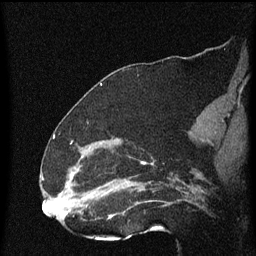
Breast MRI (dynamic contrast-enhanced), one sagittal slice. Slice 32 of 60 in the series (ordered by position). Dynamic contrast-enhanced series, image 2 of 4 at this slice position (ordered by acquisition). 1.5 T. TE 4.2 ms, TR 8 ms. 2 mm slice thickness. 256 × 256 image matrix. Patient: female, 52 years.
Annotated regions visible in this slice (semi-automatically segmented with operator editing):
- analysis volume of interest (the breast-tissue region the enhancement analysis was run in; not a lesion): bounding box (x1, y1, x2, y2) in pixels: (73, 148, 172, 219)
- tumour enhancement mask (voxels above the 70 % enhancement threshold inside the analysis volume of interest): (82, 156, 147, 219)